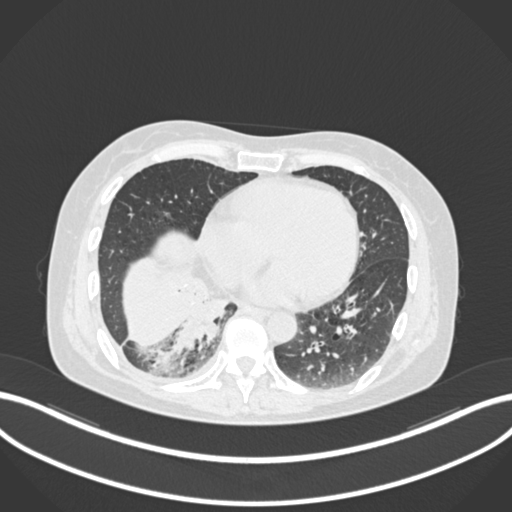
Chest CT, one axial slice; reconstruction kernel B30f; 120 kVp; lung window (W 1500 / L -600 HU); 1 mm slice thickness; 512 × 512 image matrix, field of view 400 × 400 mm. Female patient, age 63 years. Case-level facts recorded for this patient, not image findings: clinical TNM (as recorded): T1c N0 M0.
Annotated regions visible in this slice (rectangle marked by the reading radiologist):
- lung tumour (recorded histology: adenocarcinoma): bounding box [x1, y1, x2, y2] px = [164, 282, 230, 355]